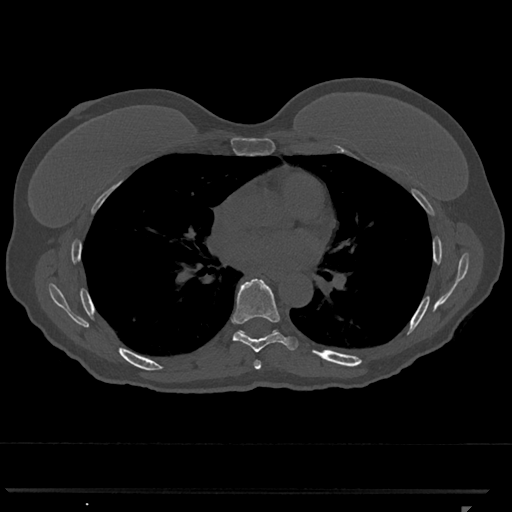
CT including the spine, one axial slice; slice 708 of 793 in the series (ordered by position); reconstruction kernel Br40s/3; 120 kVp; bone window (W 1800 / L 400 HU); 512 × 512 image matrix, field of view 380 × 380 mm. Female patient, age 62 years. From the clinical record (not read from this slice): primary cancer: renal.
Annotated regions visible in this slice (semi-automatic segmentation, software-assisted and operator-edited):
- T6 vertebra: bounding box [x1, y1, x2, y2] px = [254, 360, 262, 370]
- T7 vertebra: [225, 279, 299, 353]